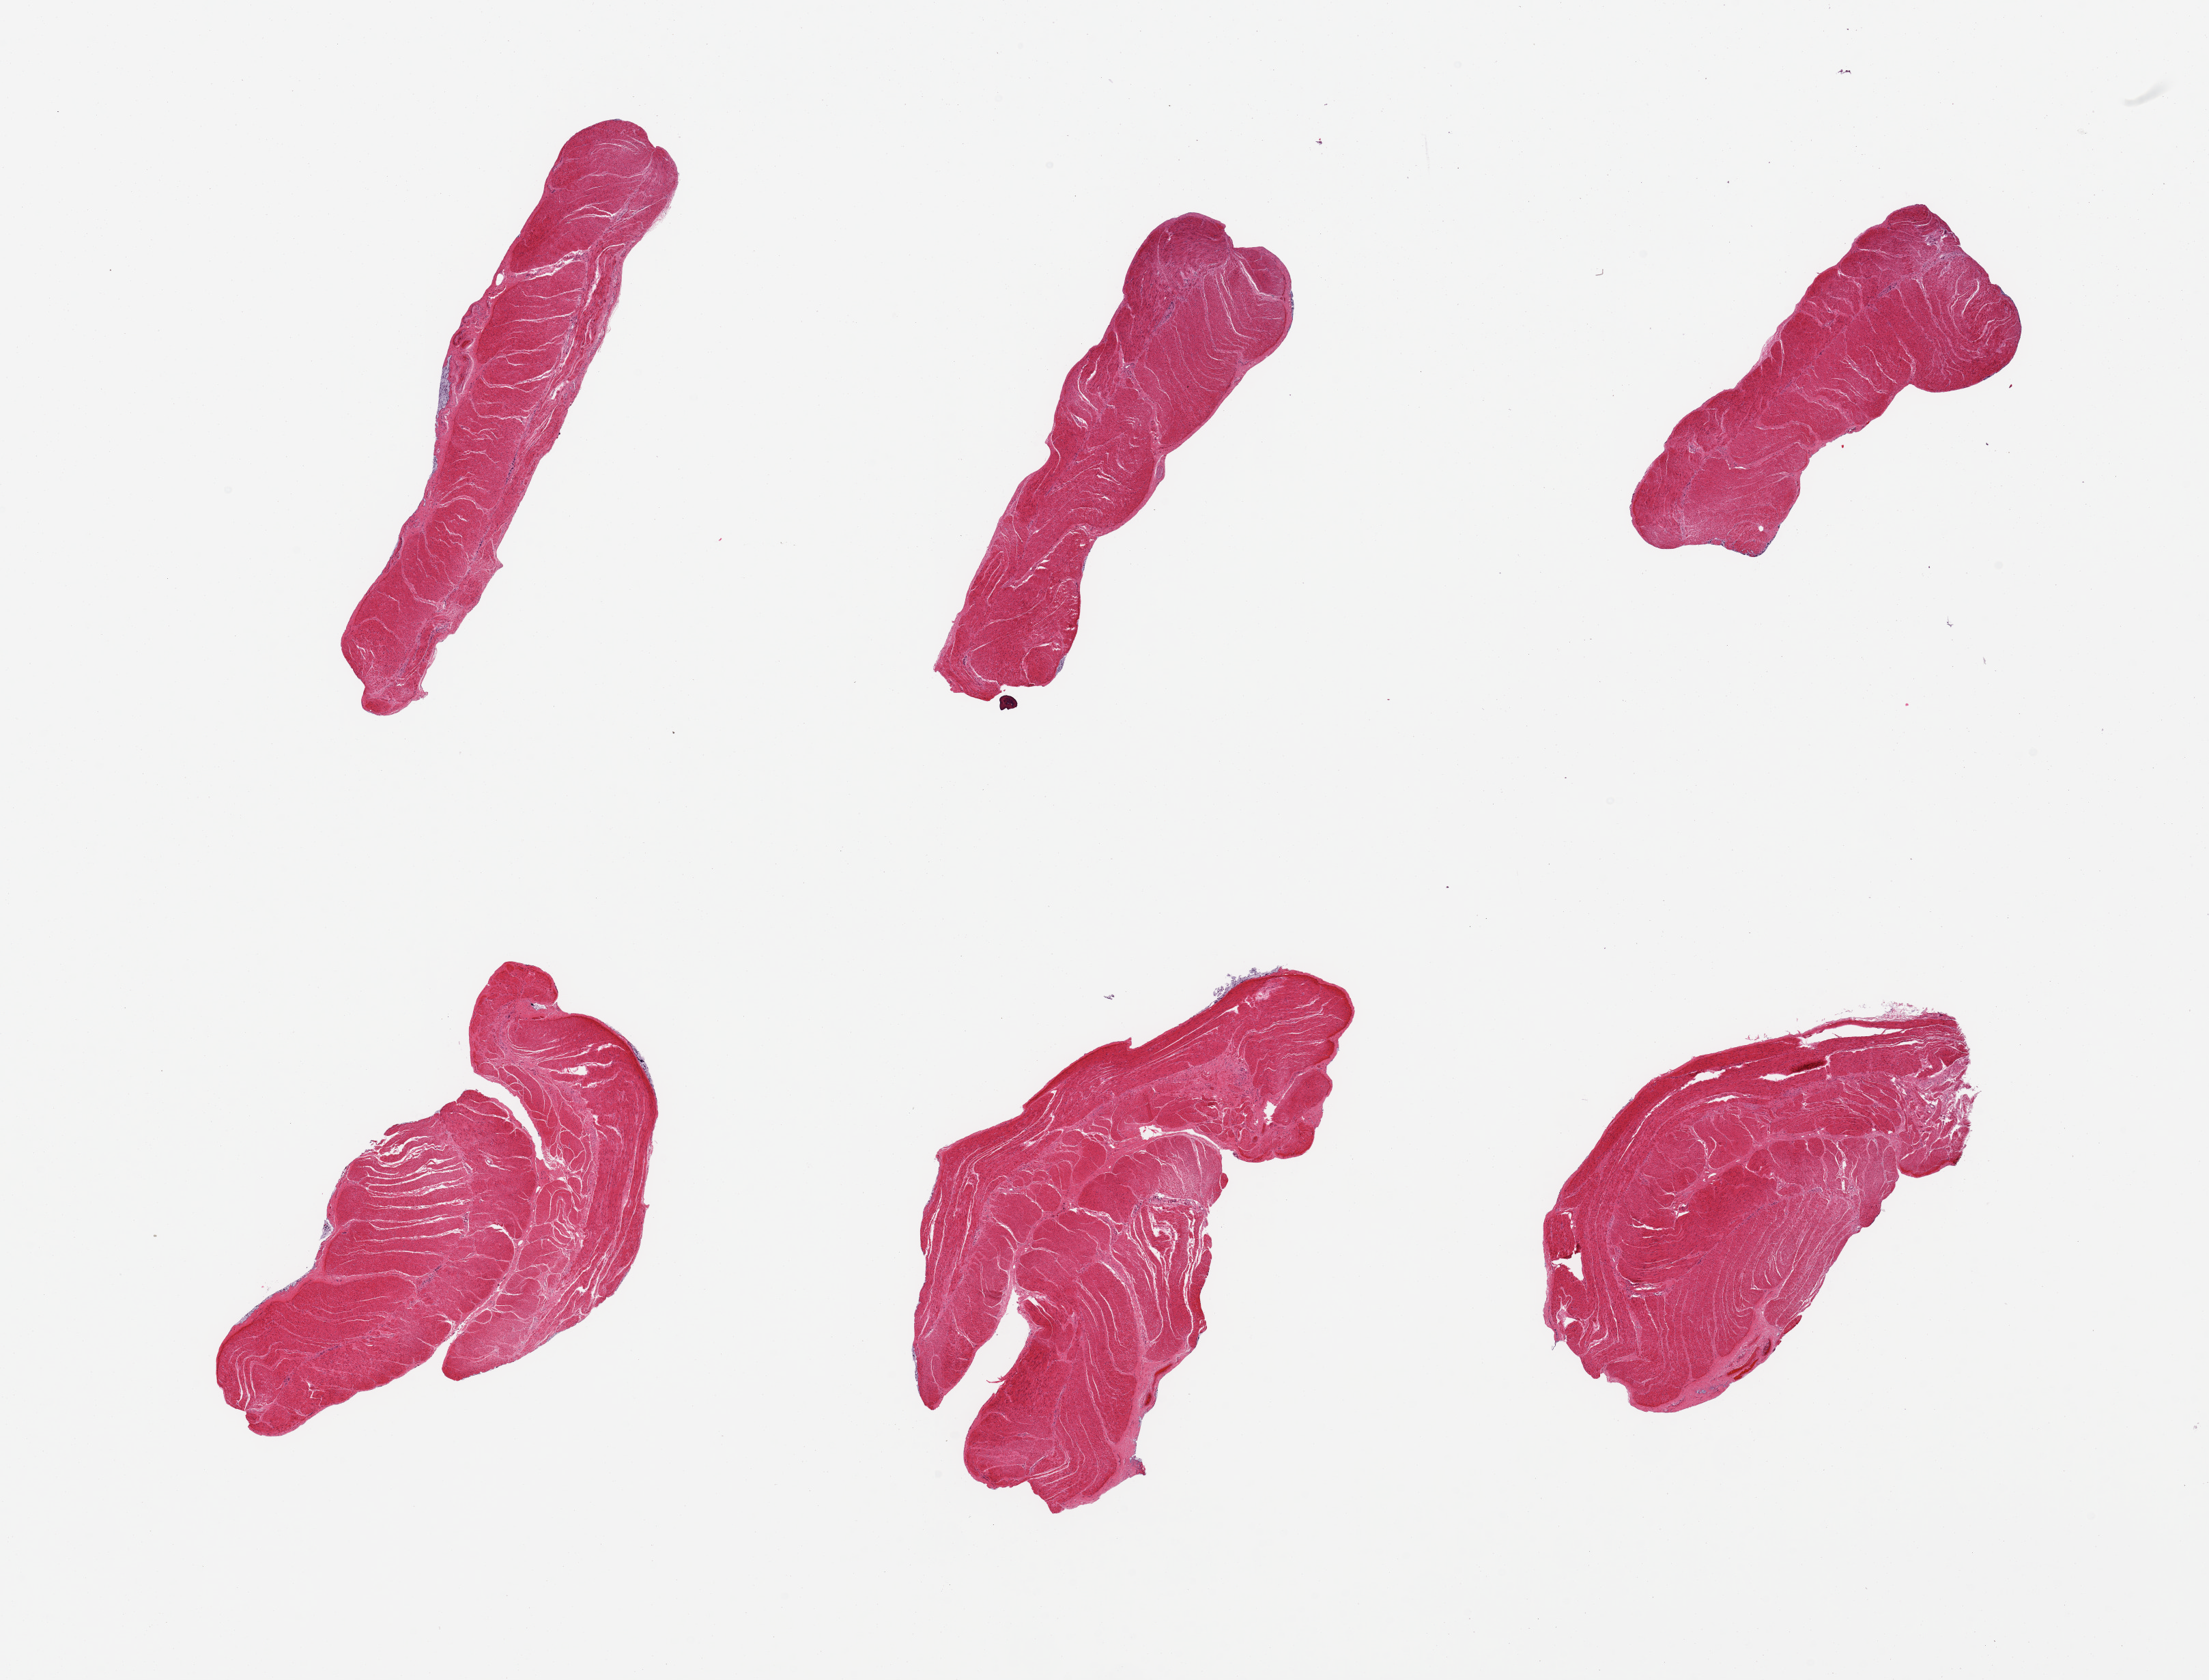
Digitized H&E-stained section — shown as a low-resolution overview of the whole scanned area (about 25.6 x 19.5 mm), PAXgene-fixed, paraffin-embedded tissue, sampled site (target tissue): sigmoid colon, tissue donor sample.
- reviewer comment on this tissue sample: 6 pieces, confirmed target muscularis